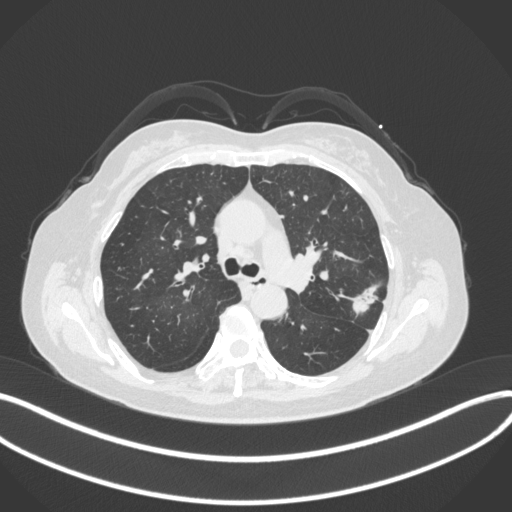
Chest CT, one axial slice. Slice 220 of 330 in the series (ordered by position). Reconstruction kernel B31f. 120 kVp. Lung window (W 1500 / L -600 HU). 1 mm slice thickness. 512 × 512 image matrix, field of view 400 × 400 mm. Patient: female, 60 years. From the clinical record (not read from this slice): clinical TNM (as recorded): T1c N0 M0.
Annotated regions visible in this slice (rectangle marked by the reading radiologist):
- lung tumour (recorded histology: adenocarcinoma): bounding box [x1, y1, x2, y2] px = [345, 278, 378, 320]